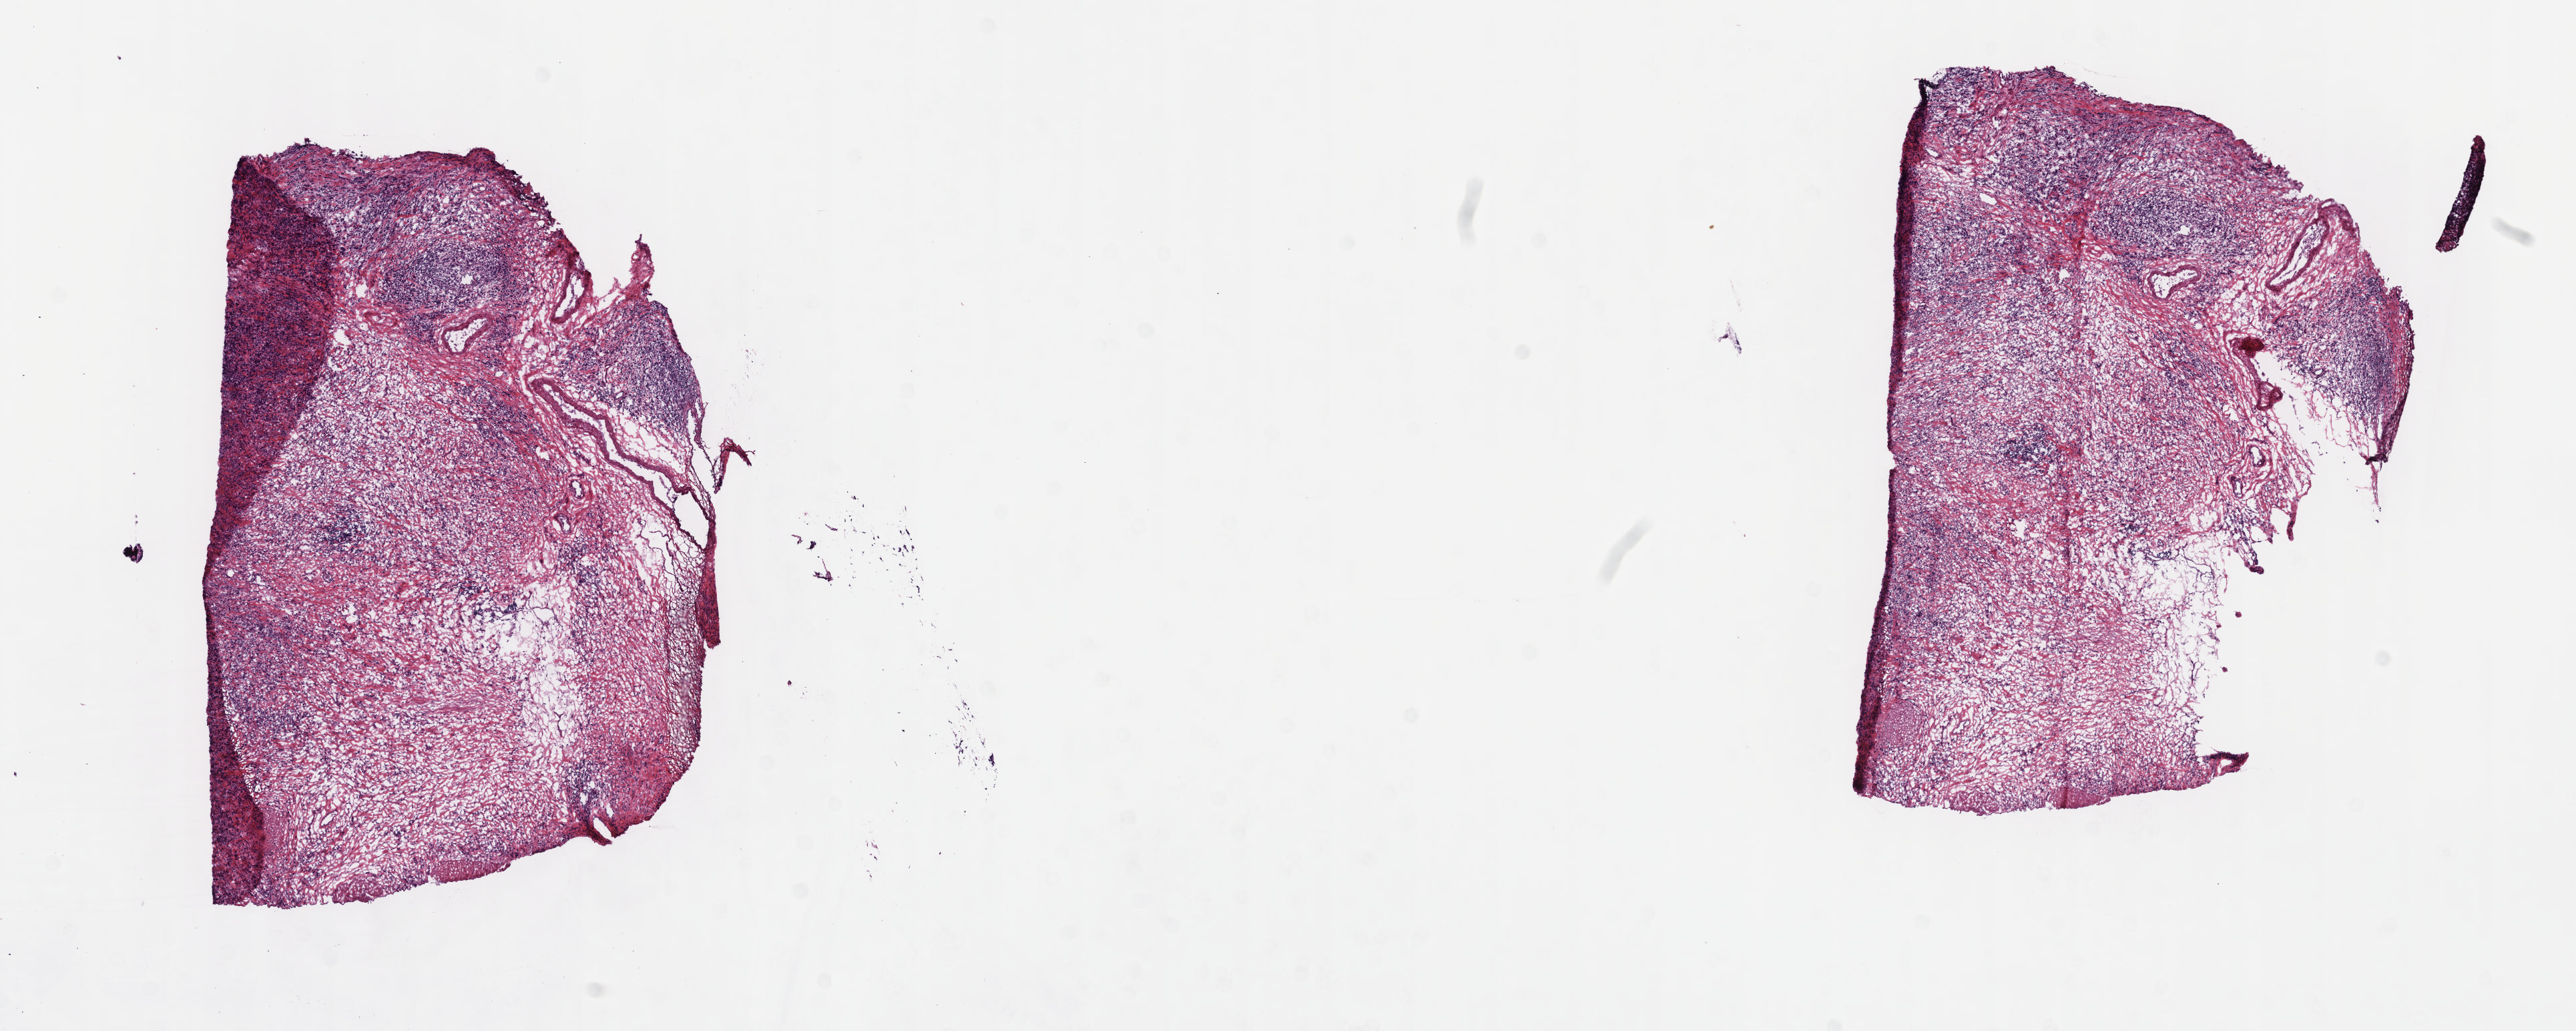
Digitized H&E-stained tissue section (whole slide), low-resolution overview of the scanned area, about 15.6 x 6.2 mm (from a 40x scan). Frozen section from the top of the tissue portion. Stomach, primary tumour sample. Male, age 51 years at initial diagnosis. Histologic grade: G3 (poorly differentiated). Slide review estimates, as recorded: tumour cells 70%, tumour nuclei 70%, normal cells 0%, stromal cells 30%, necrosis 0%. Inflammatory infiltration, as recorded: lymphocyte infiltration 40%, monocyte infiltration 20%, neutrophil infiltration 20%.
AJCC pathologic stage: IIIB. Lymph nodes positive (case pathology): 11 of 15 examined. Diagnosis: Adenocarcinoma, NOS.